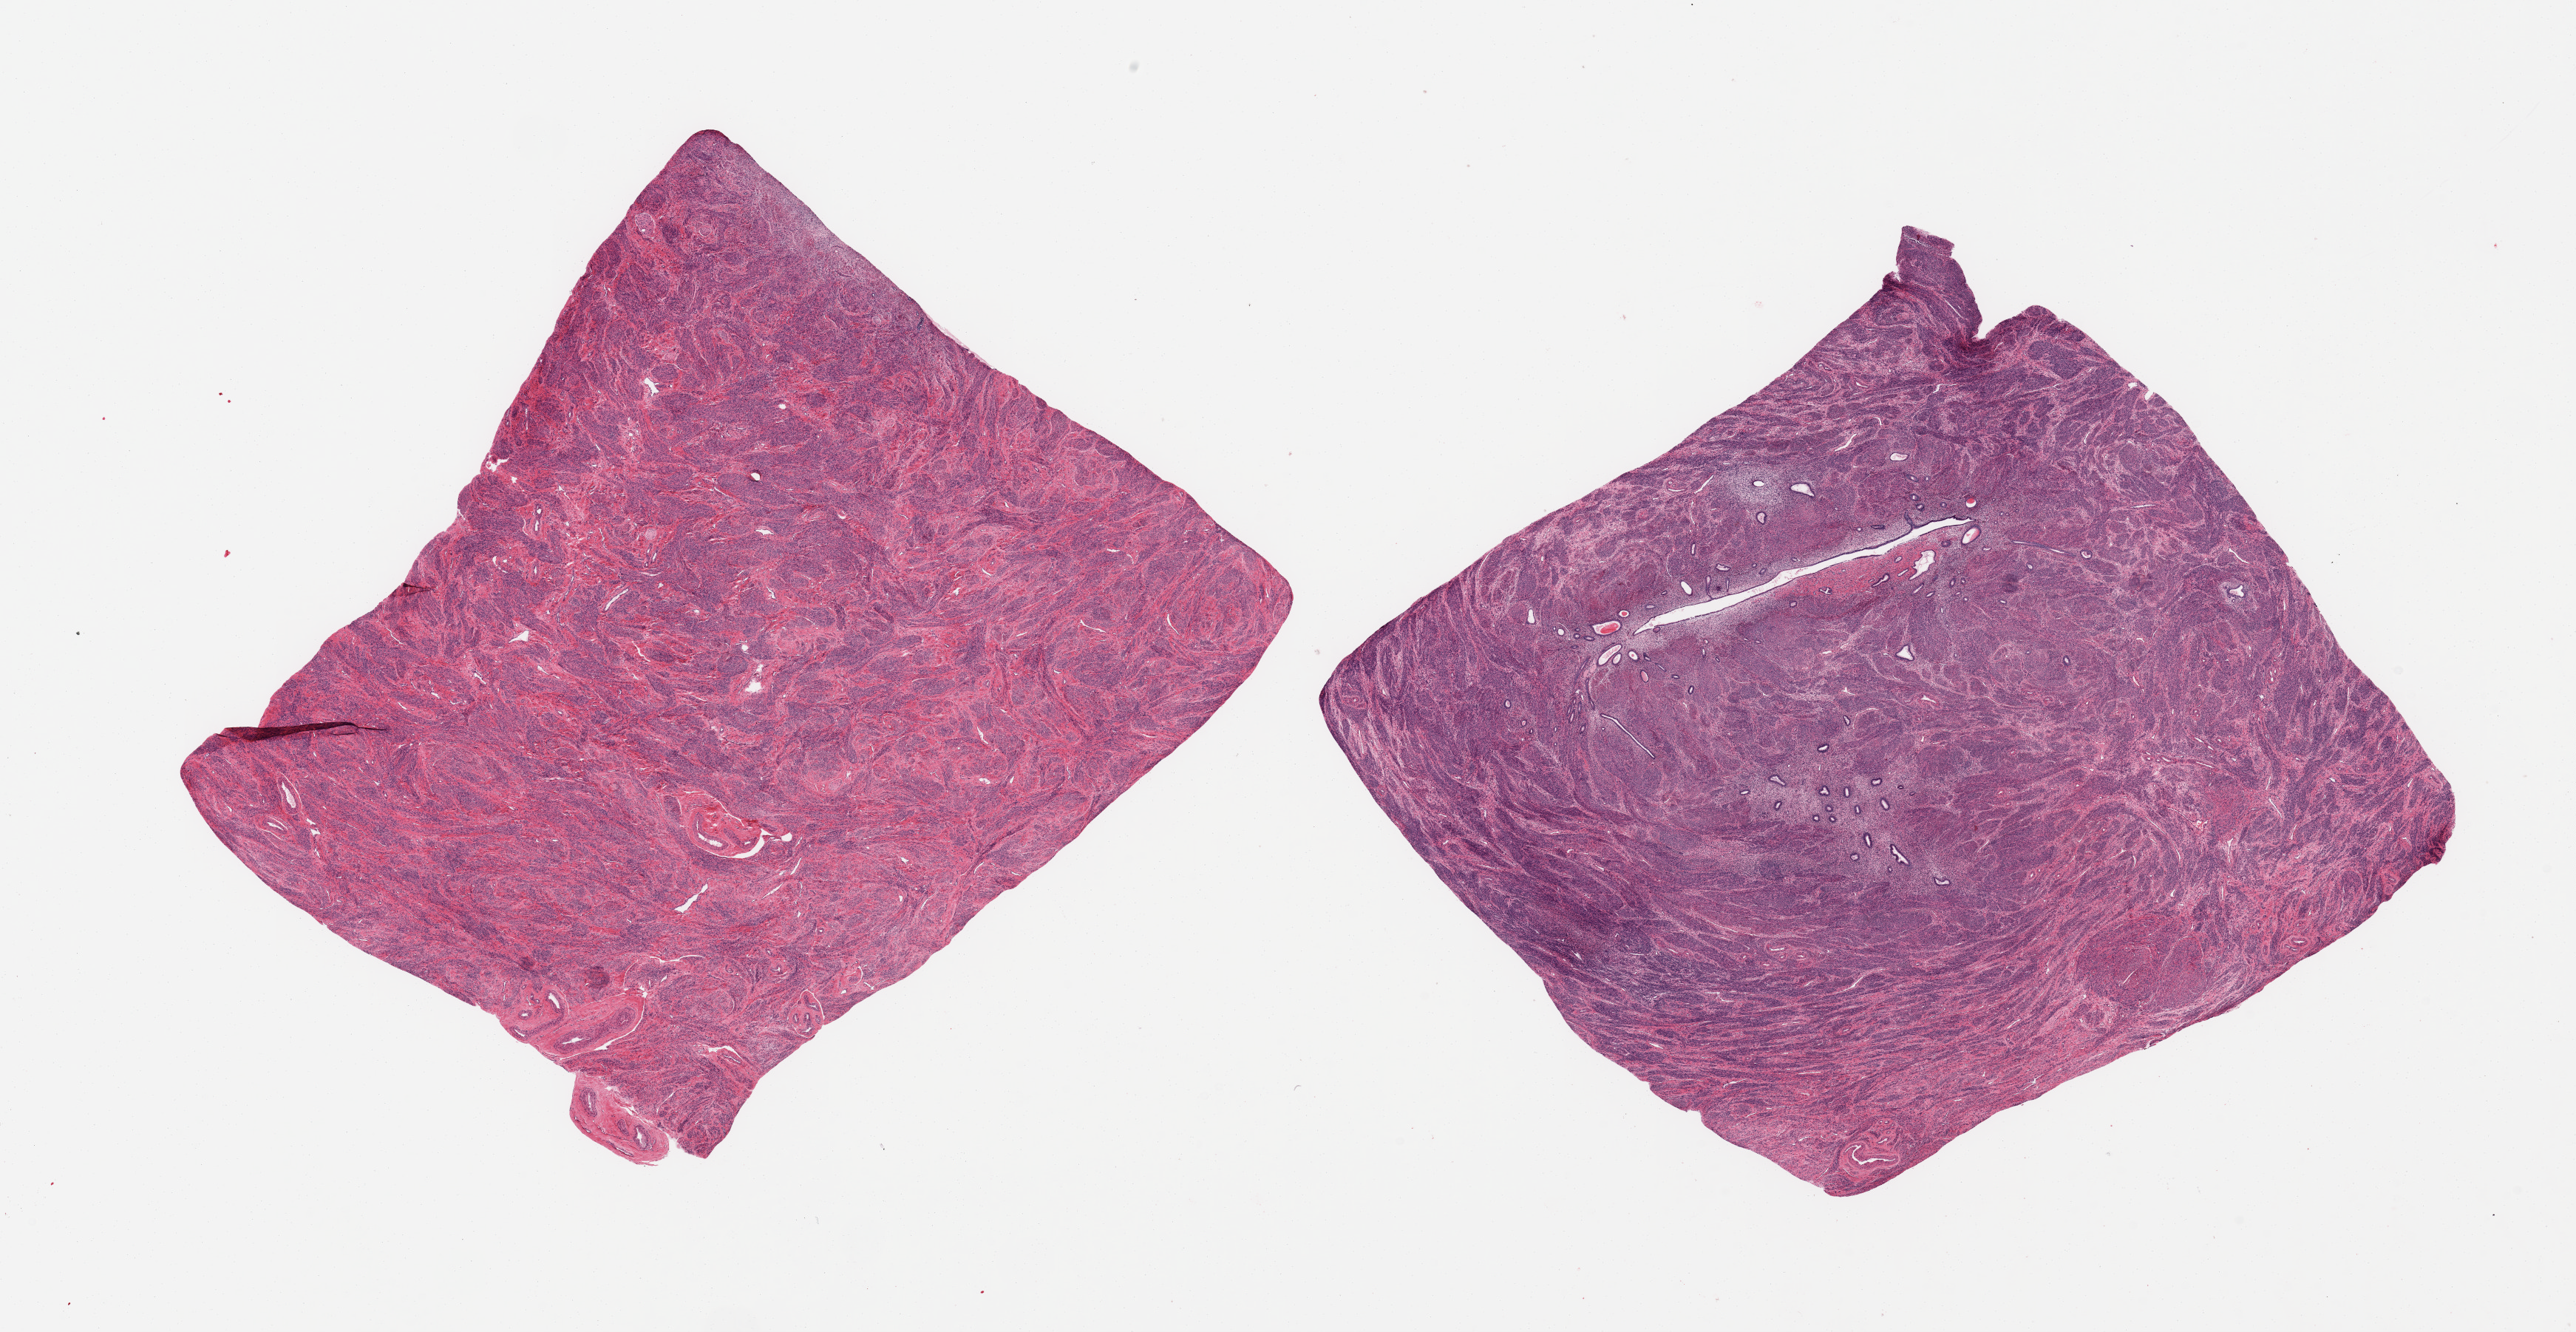
Digitized hematoxylin and eosin (H&E)-stained section — shown as a low-resolution overview of the whole scanned area (about 27.6 x 14.3 mm); PAXgene-fixed, paraffin-embedded tissue; section of uterus (target tissue); donor tissue sample.
- reviewer comment on this tissue sample: 2 pieces; mostly myometrium, one piece contains atrophic endometrial glands